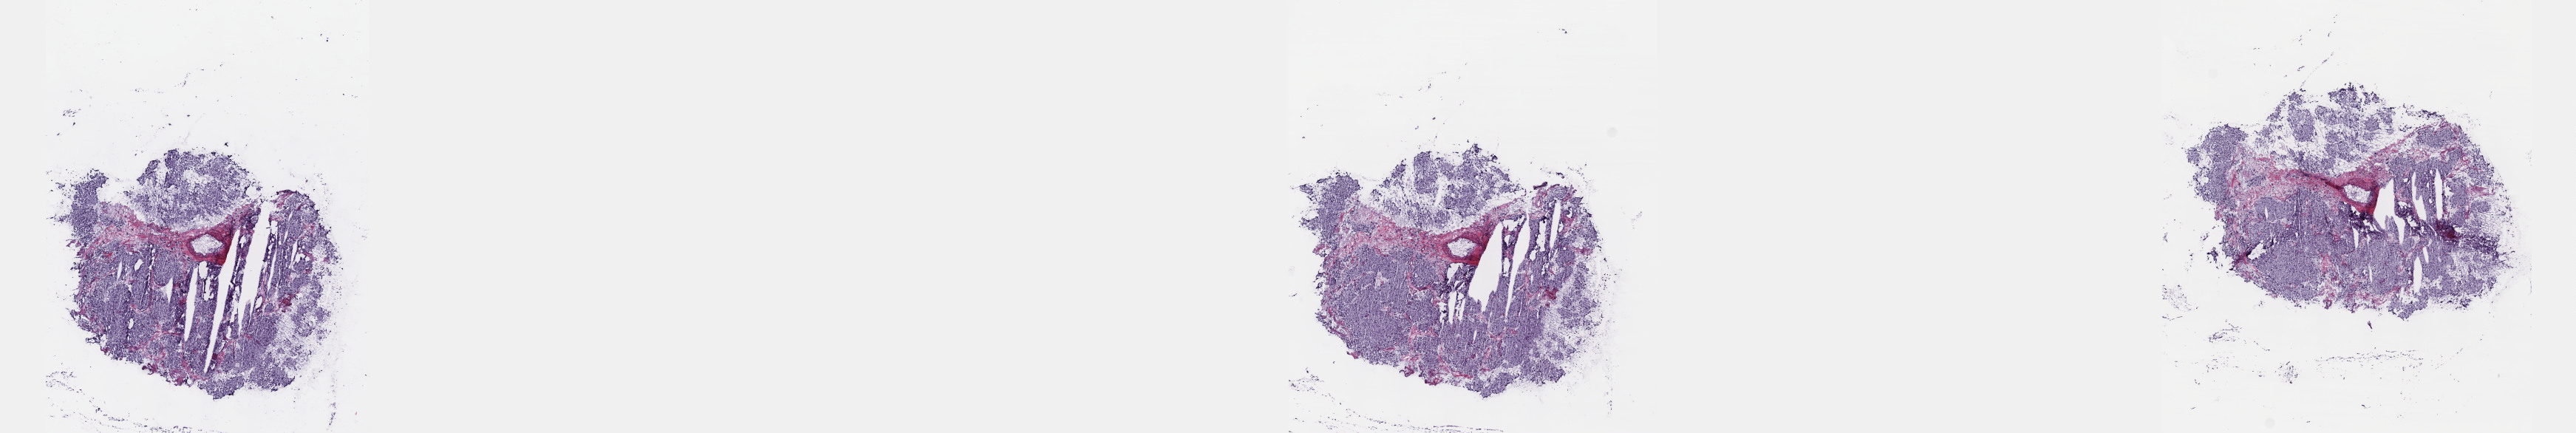
Digitized H&E tissue section (whole slide) — low-resolution overview of the scanned area, about 28.2 x 4.7 mm (slide scanned at 40x). Frozen section from the top of the tissue portion. Sample: primary tumour, adrenal gland. Patient: female, age at initial diagnosis 63 years. Composition of this section per pathologist review: tumour cells 99%, tumour nuclei 99%, normal cells 0%, stromal cells 1%, necrosis 0%. Infiltration values recorded for this section: lymphocyte infiltration 0%, monocyte infiltration 0%, neutrophil infiltration 0%.
Laterality: right. Pathologic diagnosis: Pheochromocytoma, NOS.